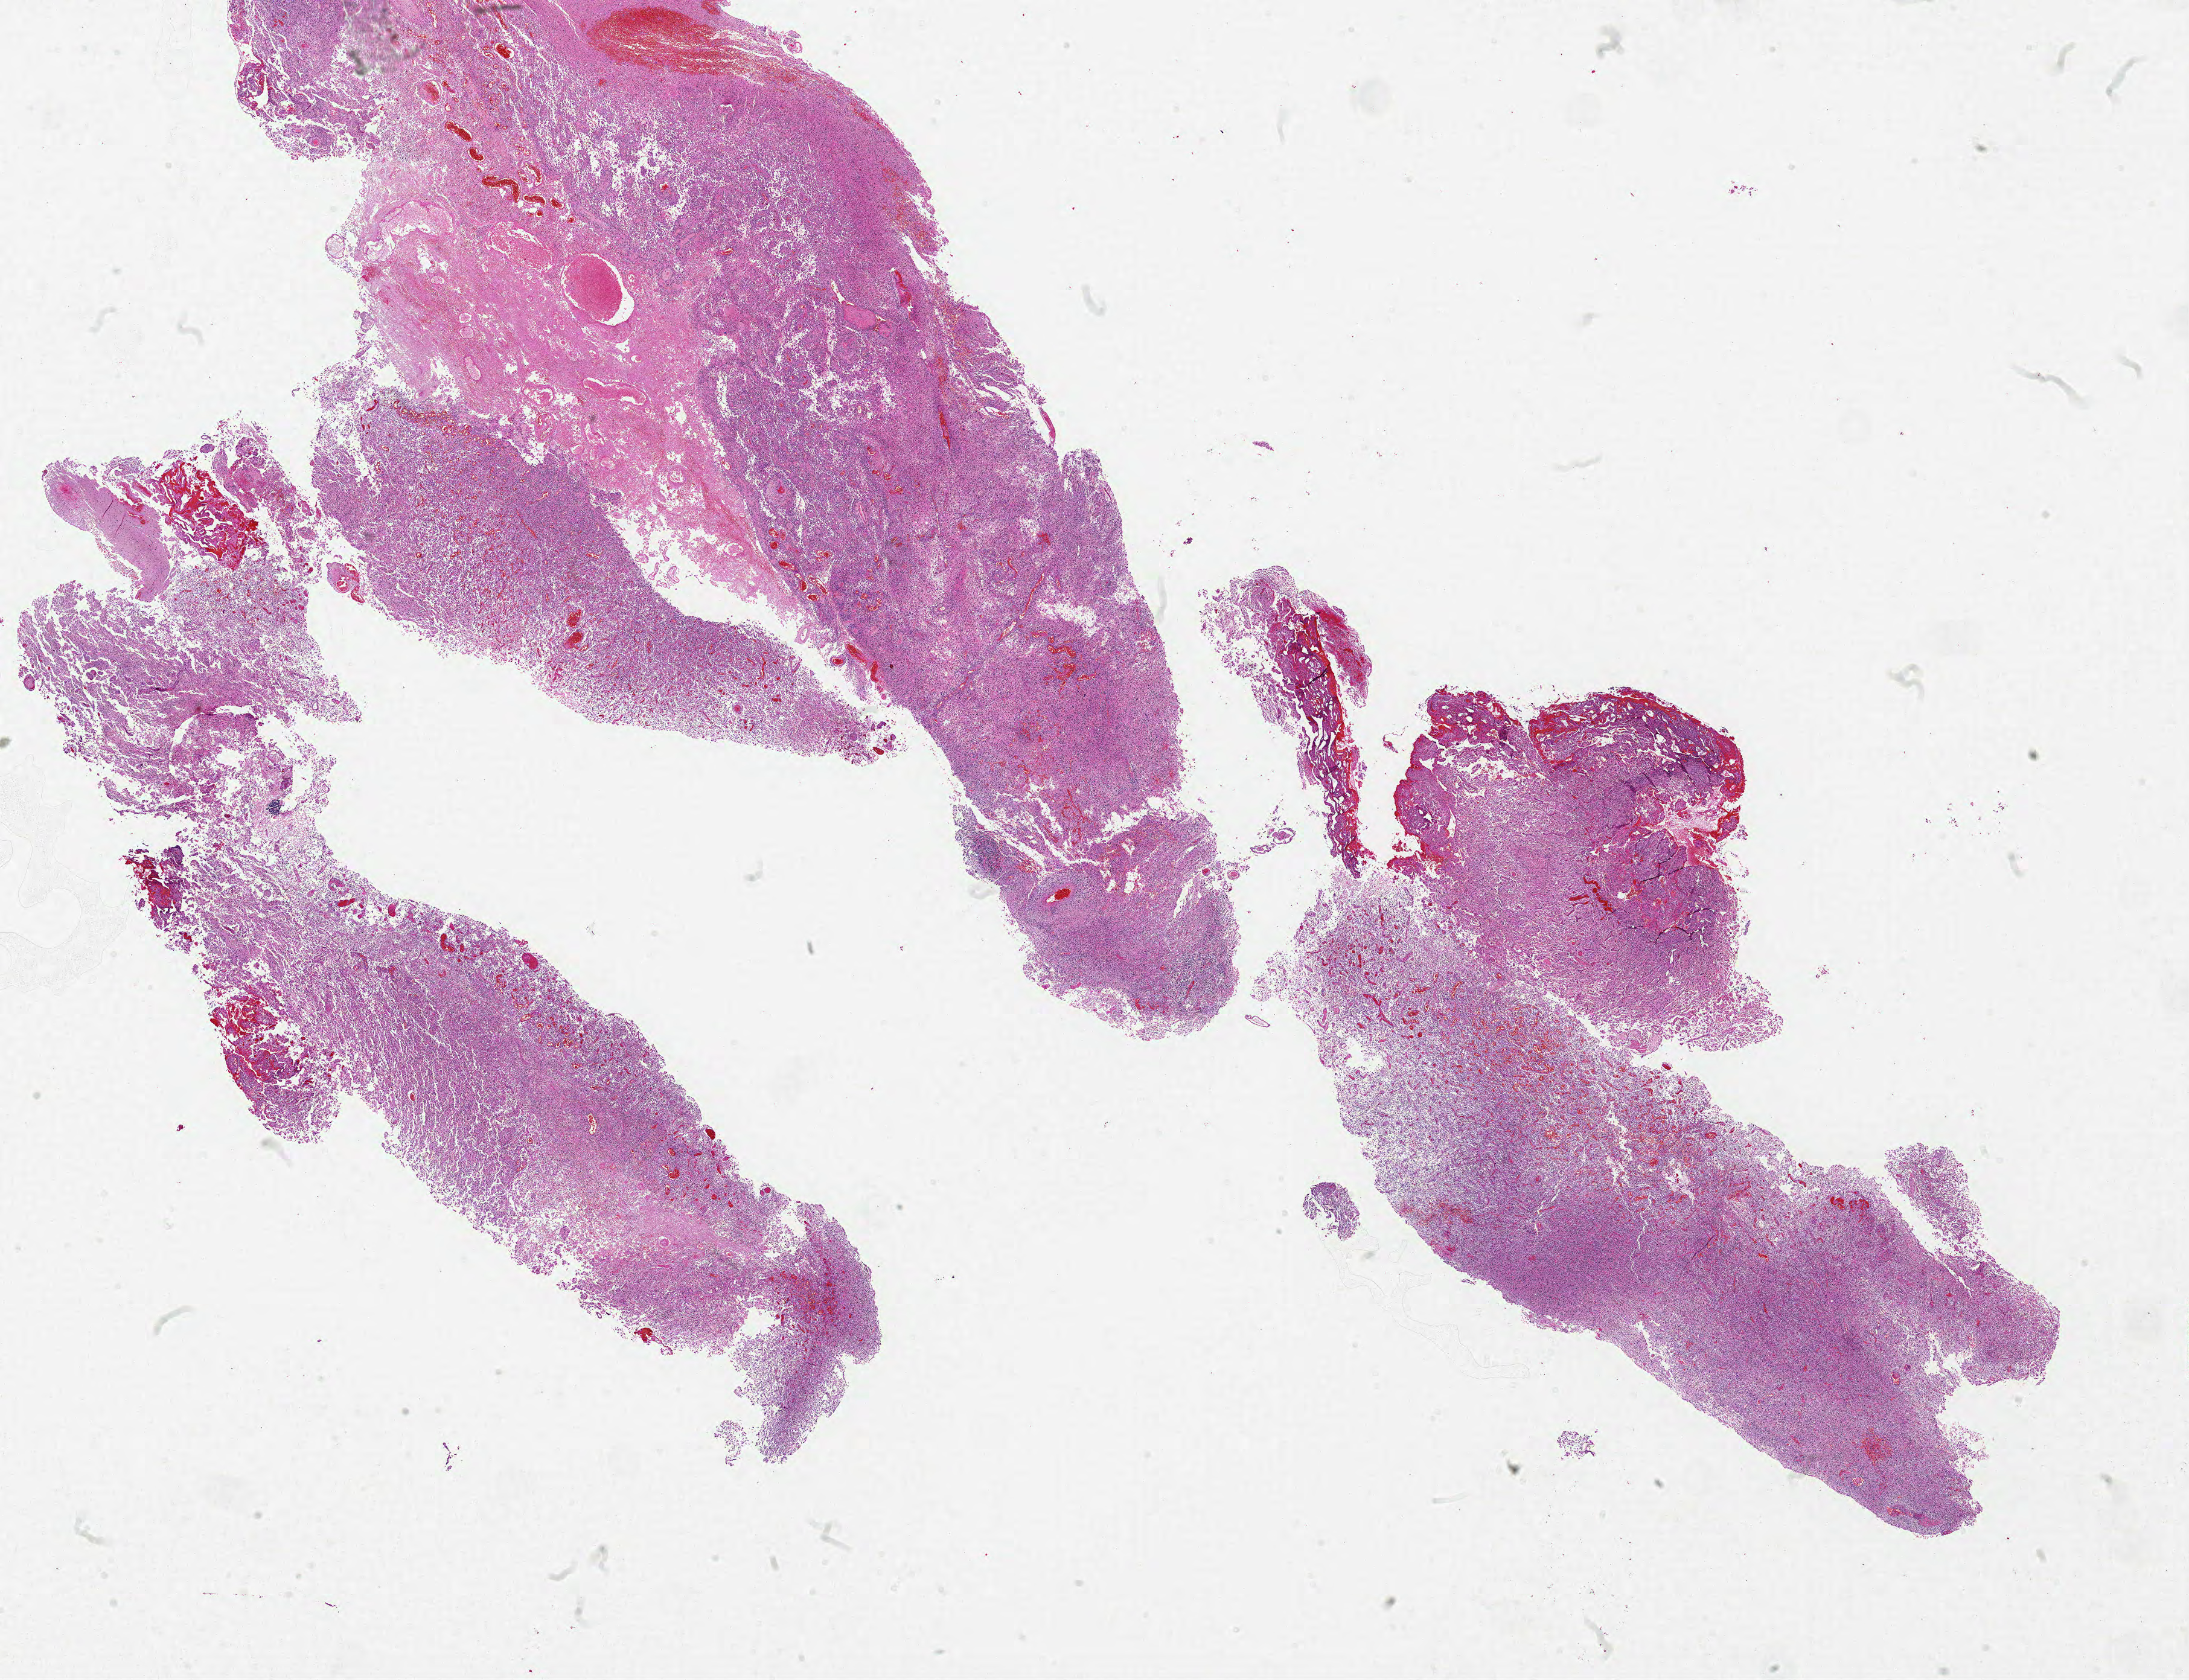
Hematoxylin and eosin (H&E) stained whole-slide image — low-resolution overview of the scanned area, about 29.0 x 22.2 mm (from a 20x scan), formalin-fixed paraffin-embedded (FFPE) diagnostic section, primary tumour sample from the brain. Male, age 46 years at initial diagnosis.
• histologic diagnosis: Glioblastoma